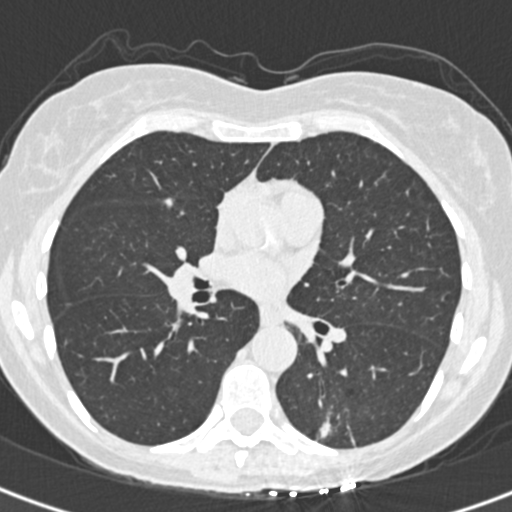
Low-dose screening chest CT, one axial slice; position 185 of 328 along the scan axis; reconstruction kernel B30f; 120 kVp; lung window (W 1500 / L -600 HU); 512 × 512 image matrix.
Structures marked on this image (manually delineated by an expert):
- lesion 1 (tumor, lower lobe of left lung): bounding box (x1, y1, x2, y2) in pixels: (320, 419, 331, 438)